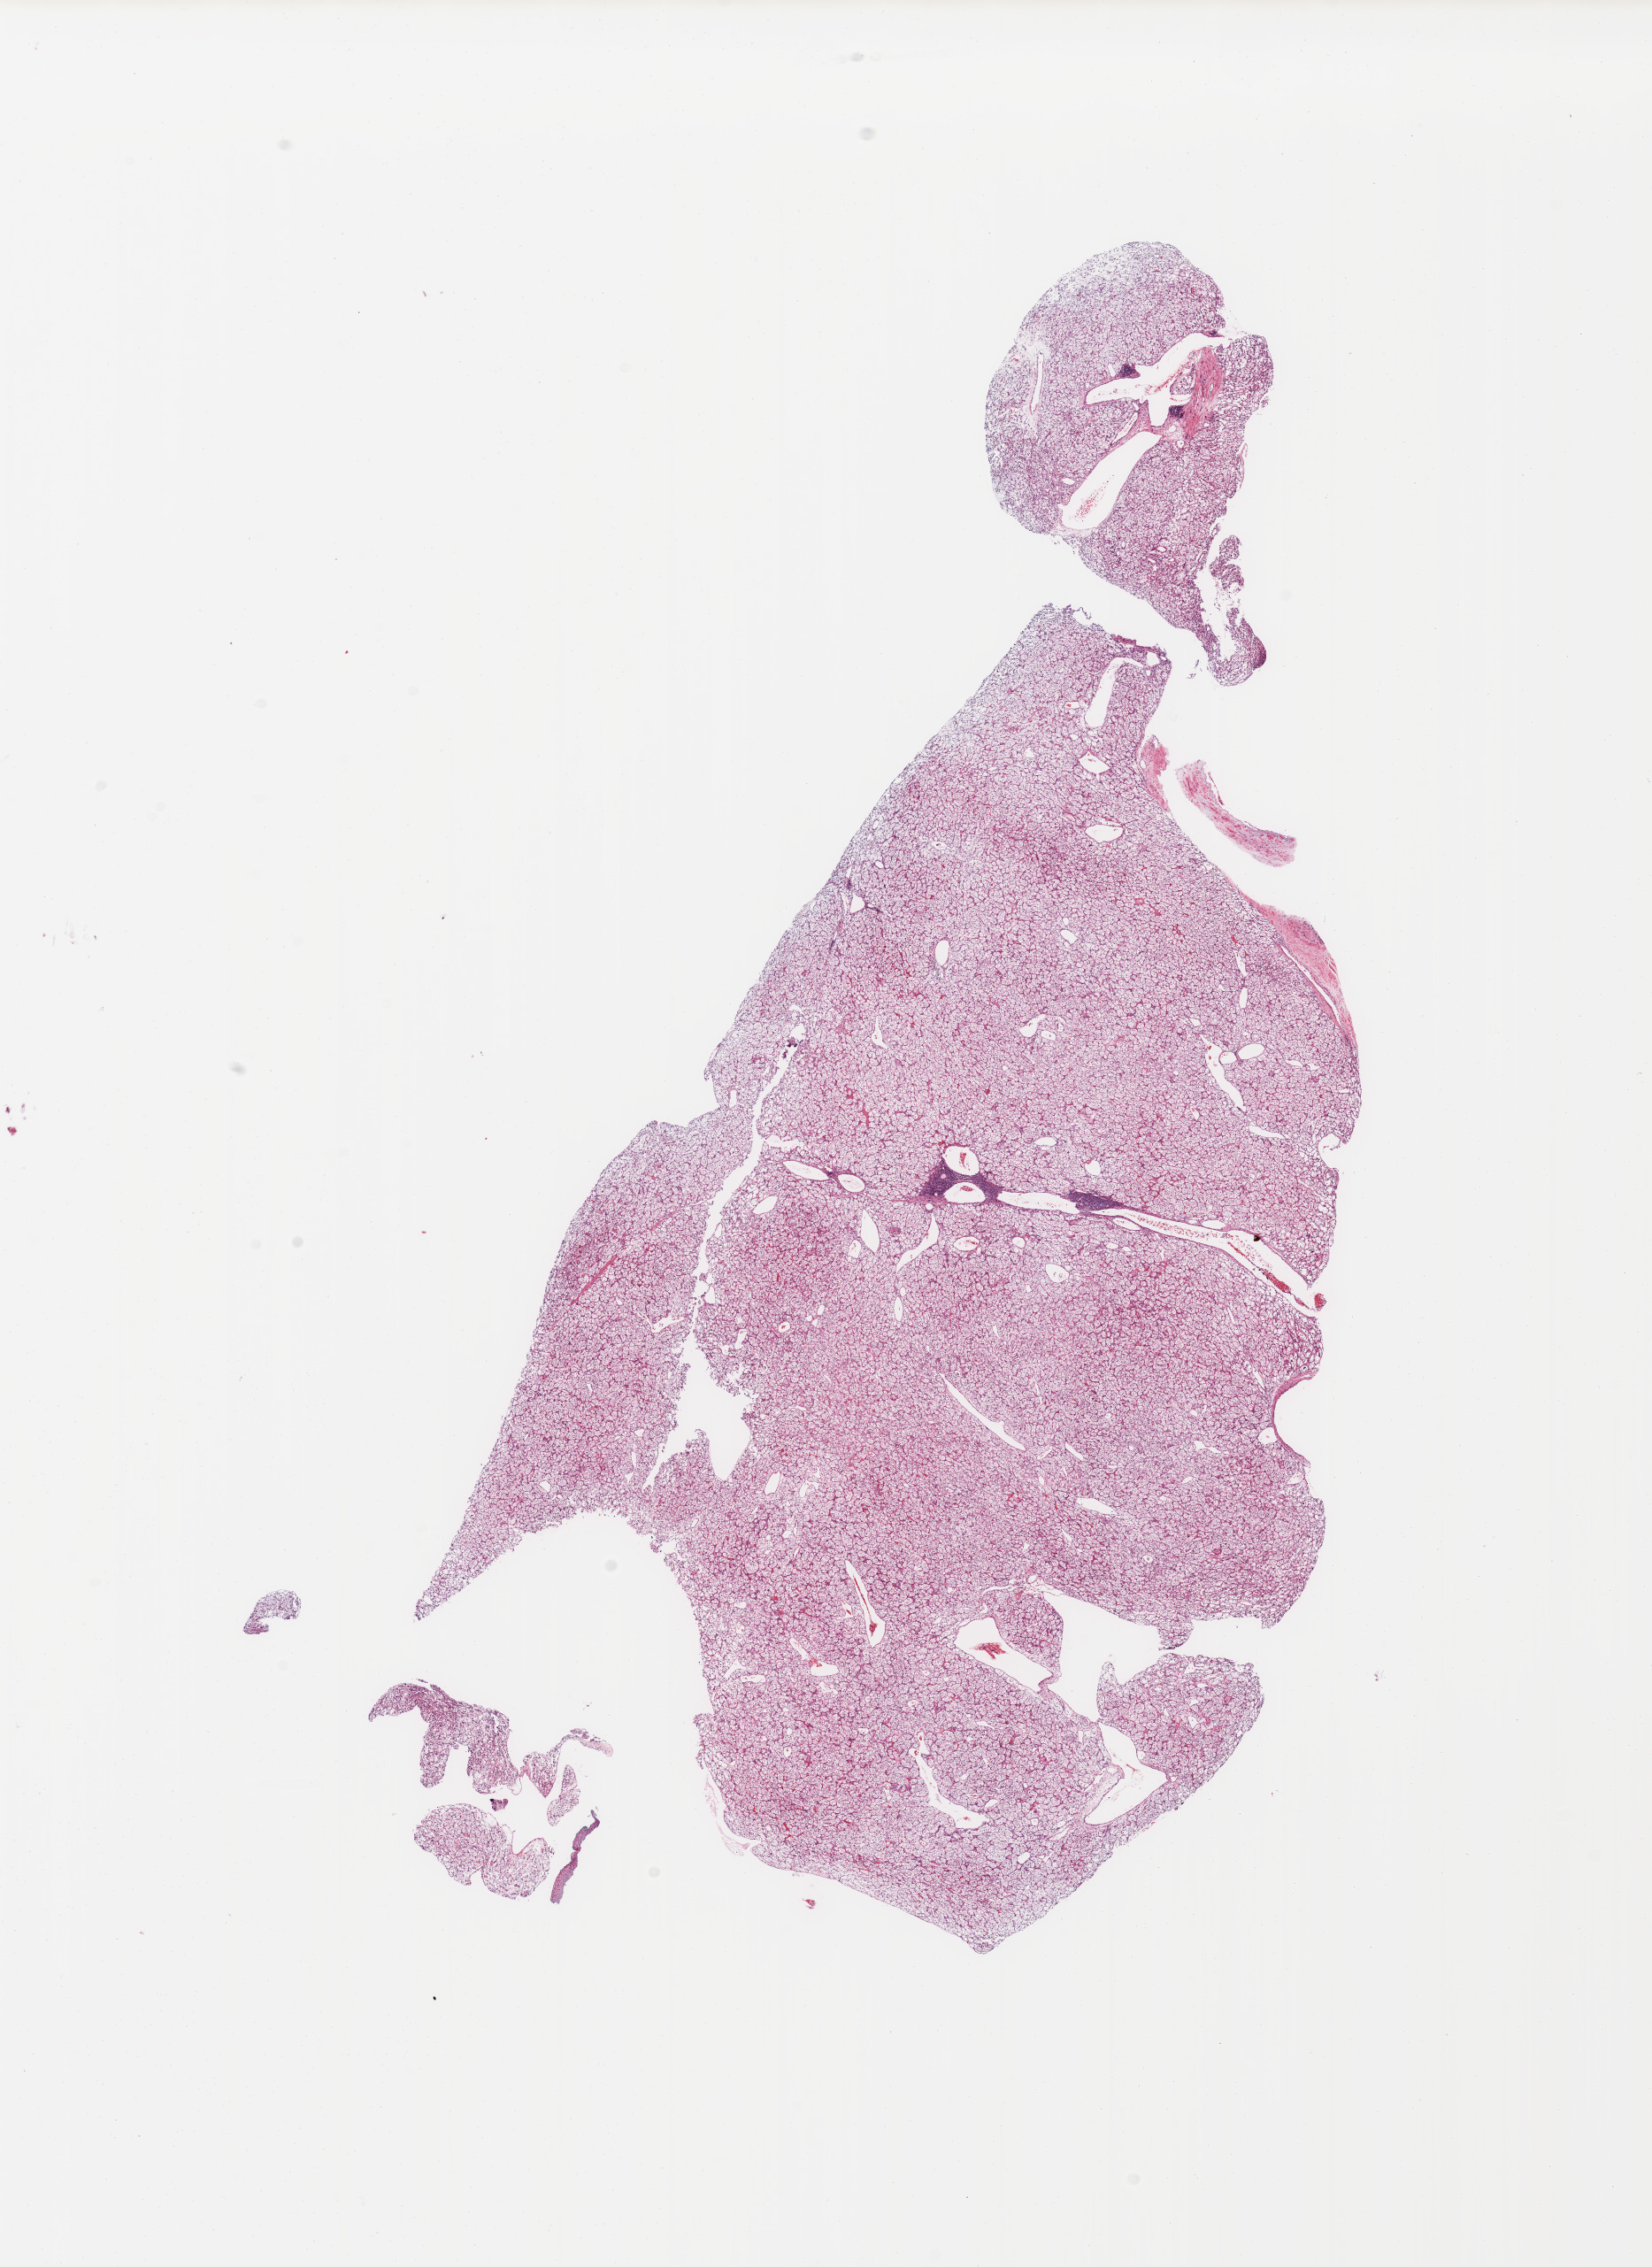
Hematoxylin and eosin (H&E) stained whole-slide image — low-resolution overview of the scanned area, about 14.8 x 20.3 mm (from a 20x scan). Tumour tissue sample, kidney. Patient: female, age 72 years. Histologic grade: G4 (undifferentiated).
Primary tumour site (as recorded): middle. Diagnosis: Renal cell carcinoma, NOS. AJCC pathologic stage: III.